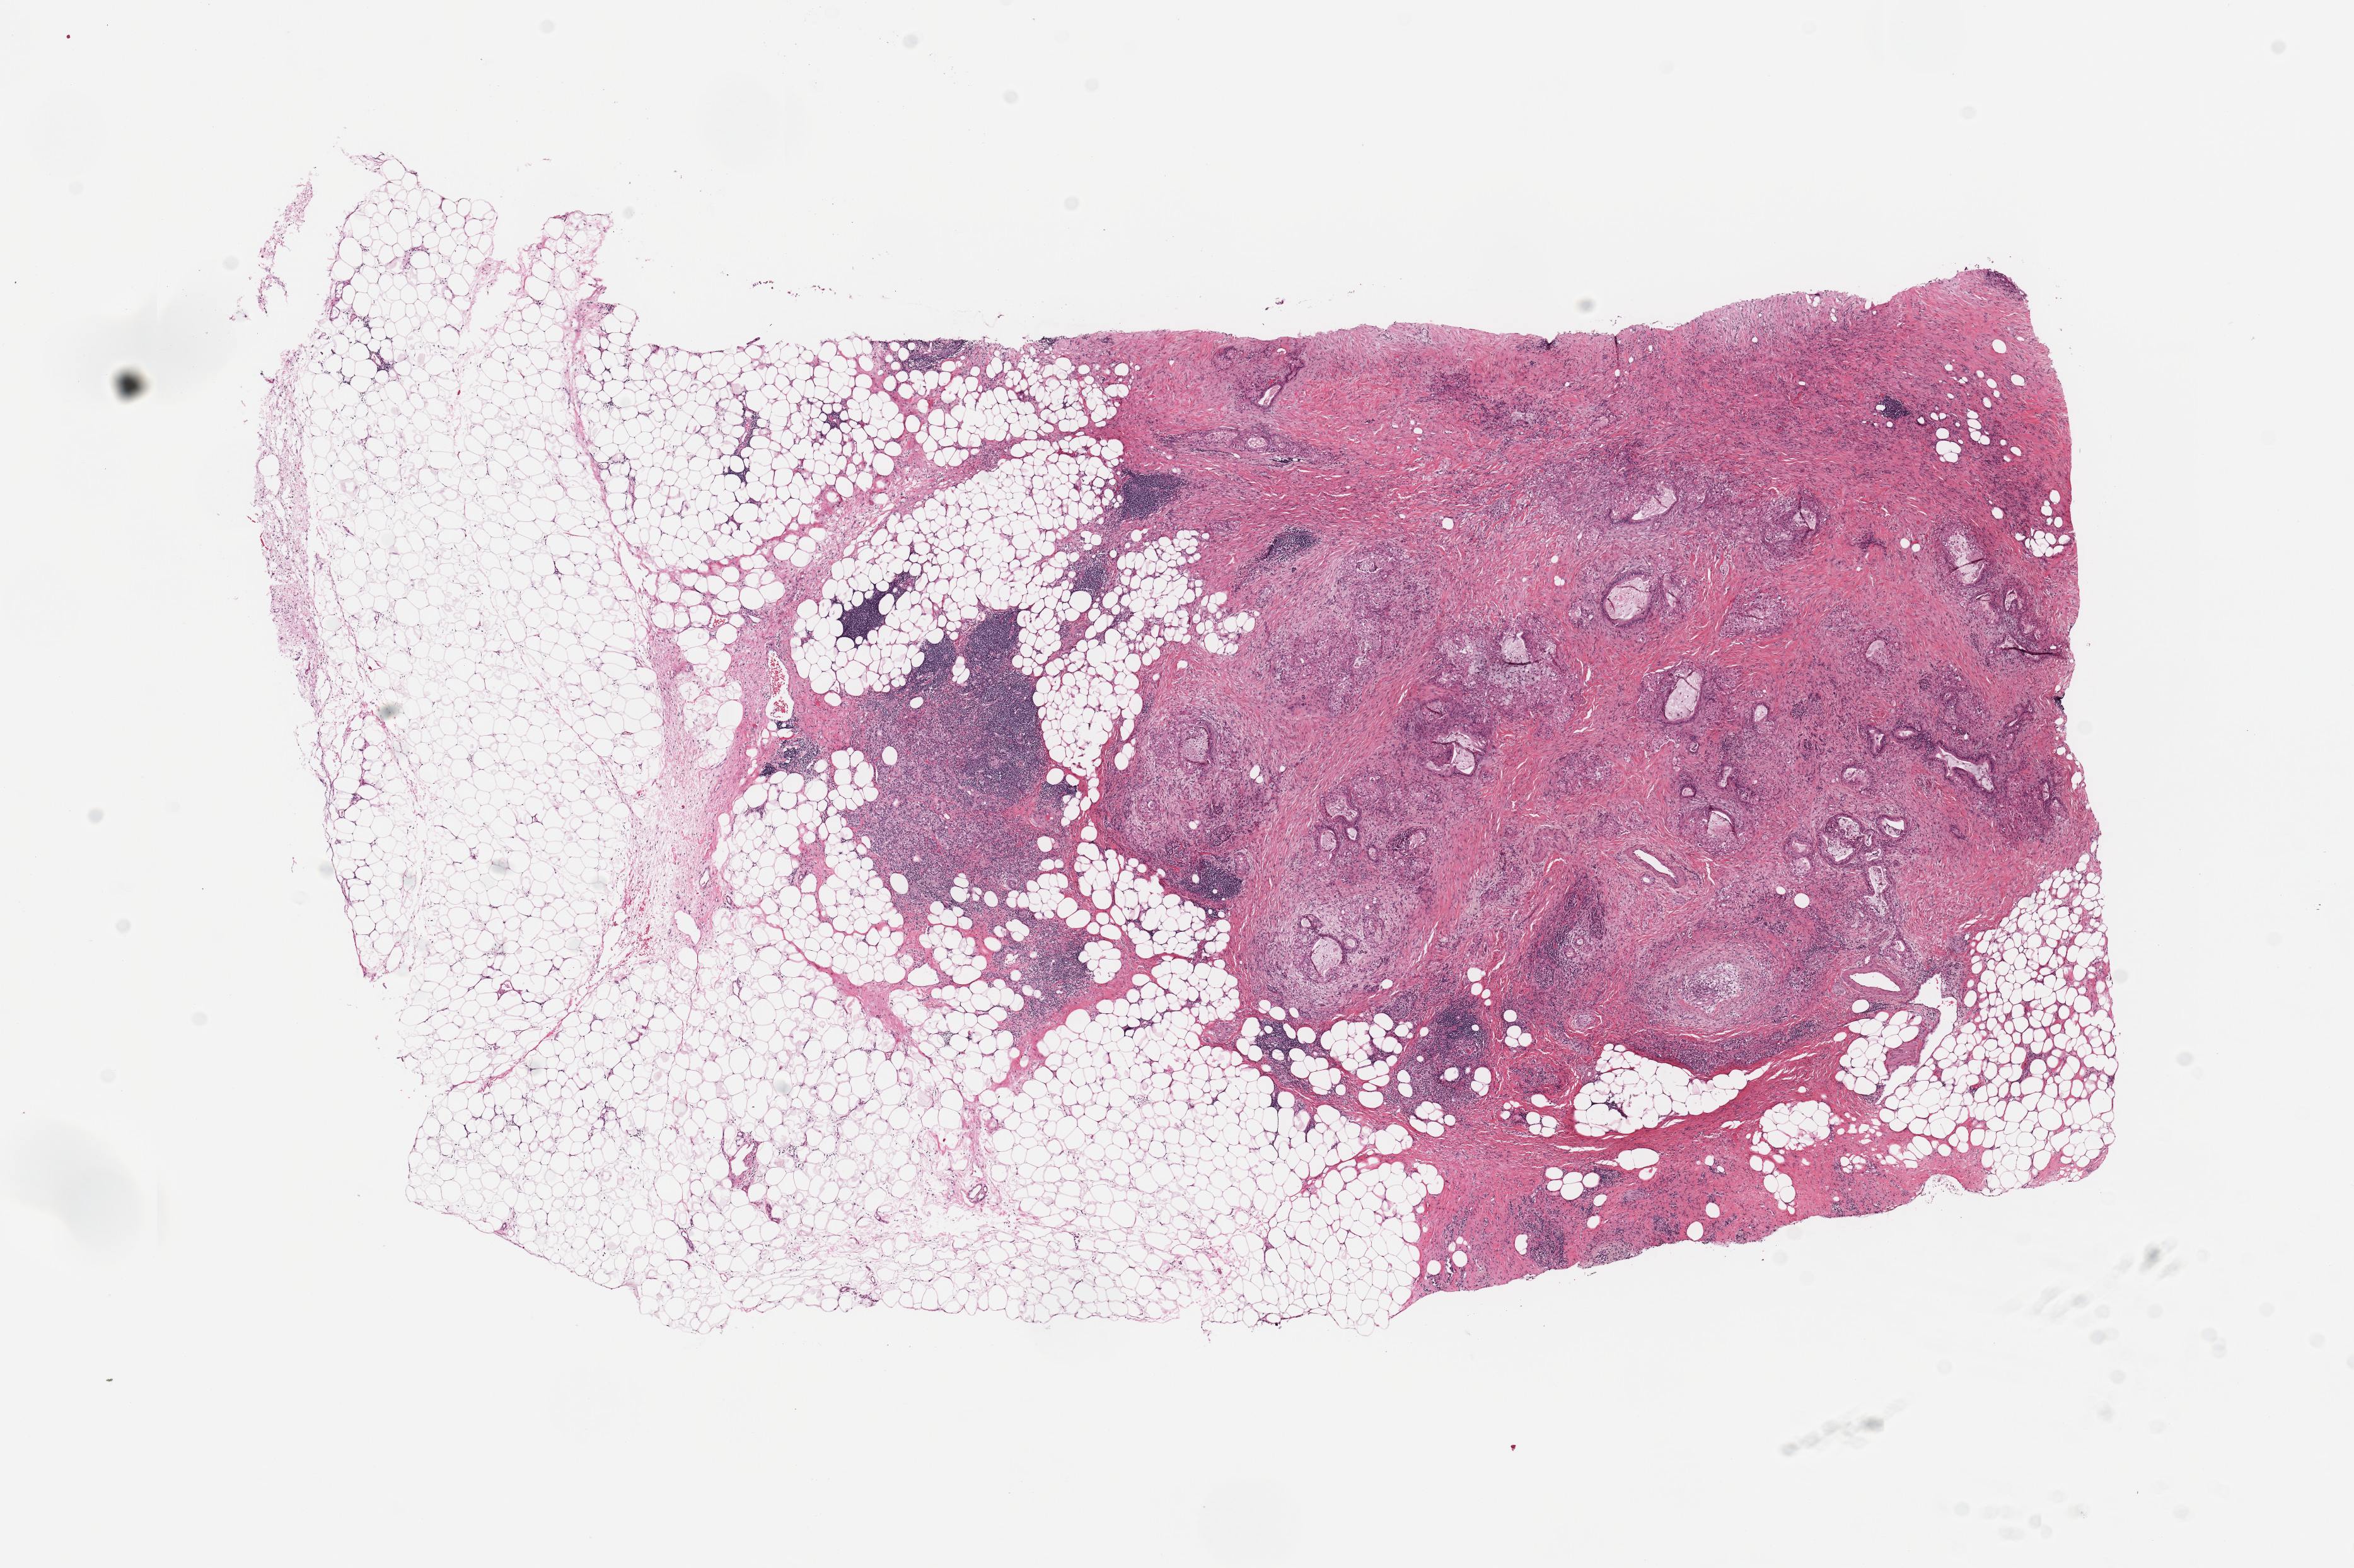
H&E whole-slide image, shown as a low-resolution overview of the whole scanned area (about 14.8 x 9.8 mm, acquisition: 20x scan), tumour tissue sample, pancreas. Female, 65 y/o. Histologic grade: G1 (well differentiated).
Primary tumour site (as recorded): body. Histologic diagnosis: Infiltrating duct carcinoma, NOS. AJCC pathologic stage: IA.